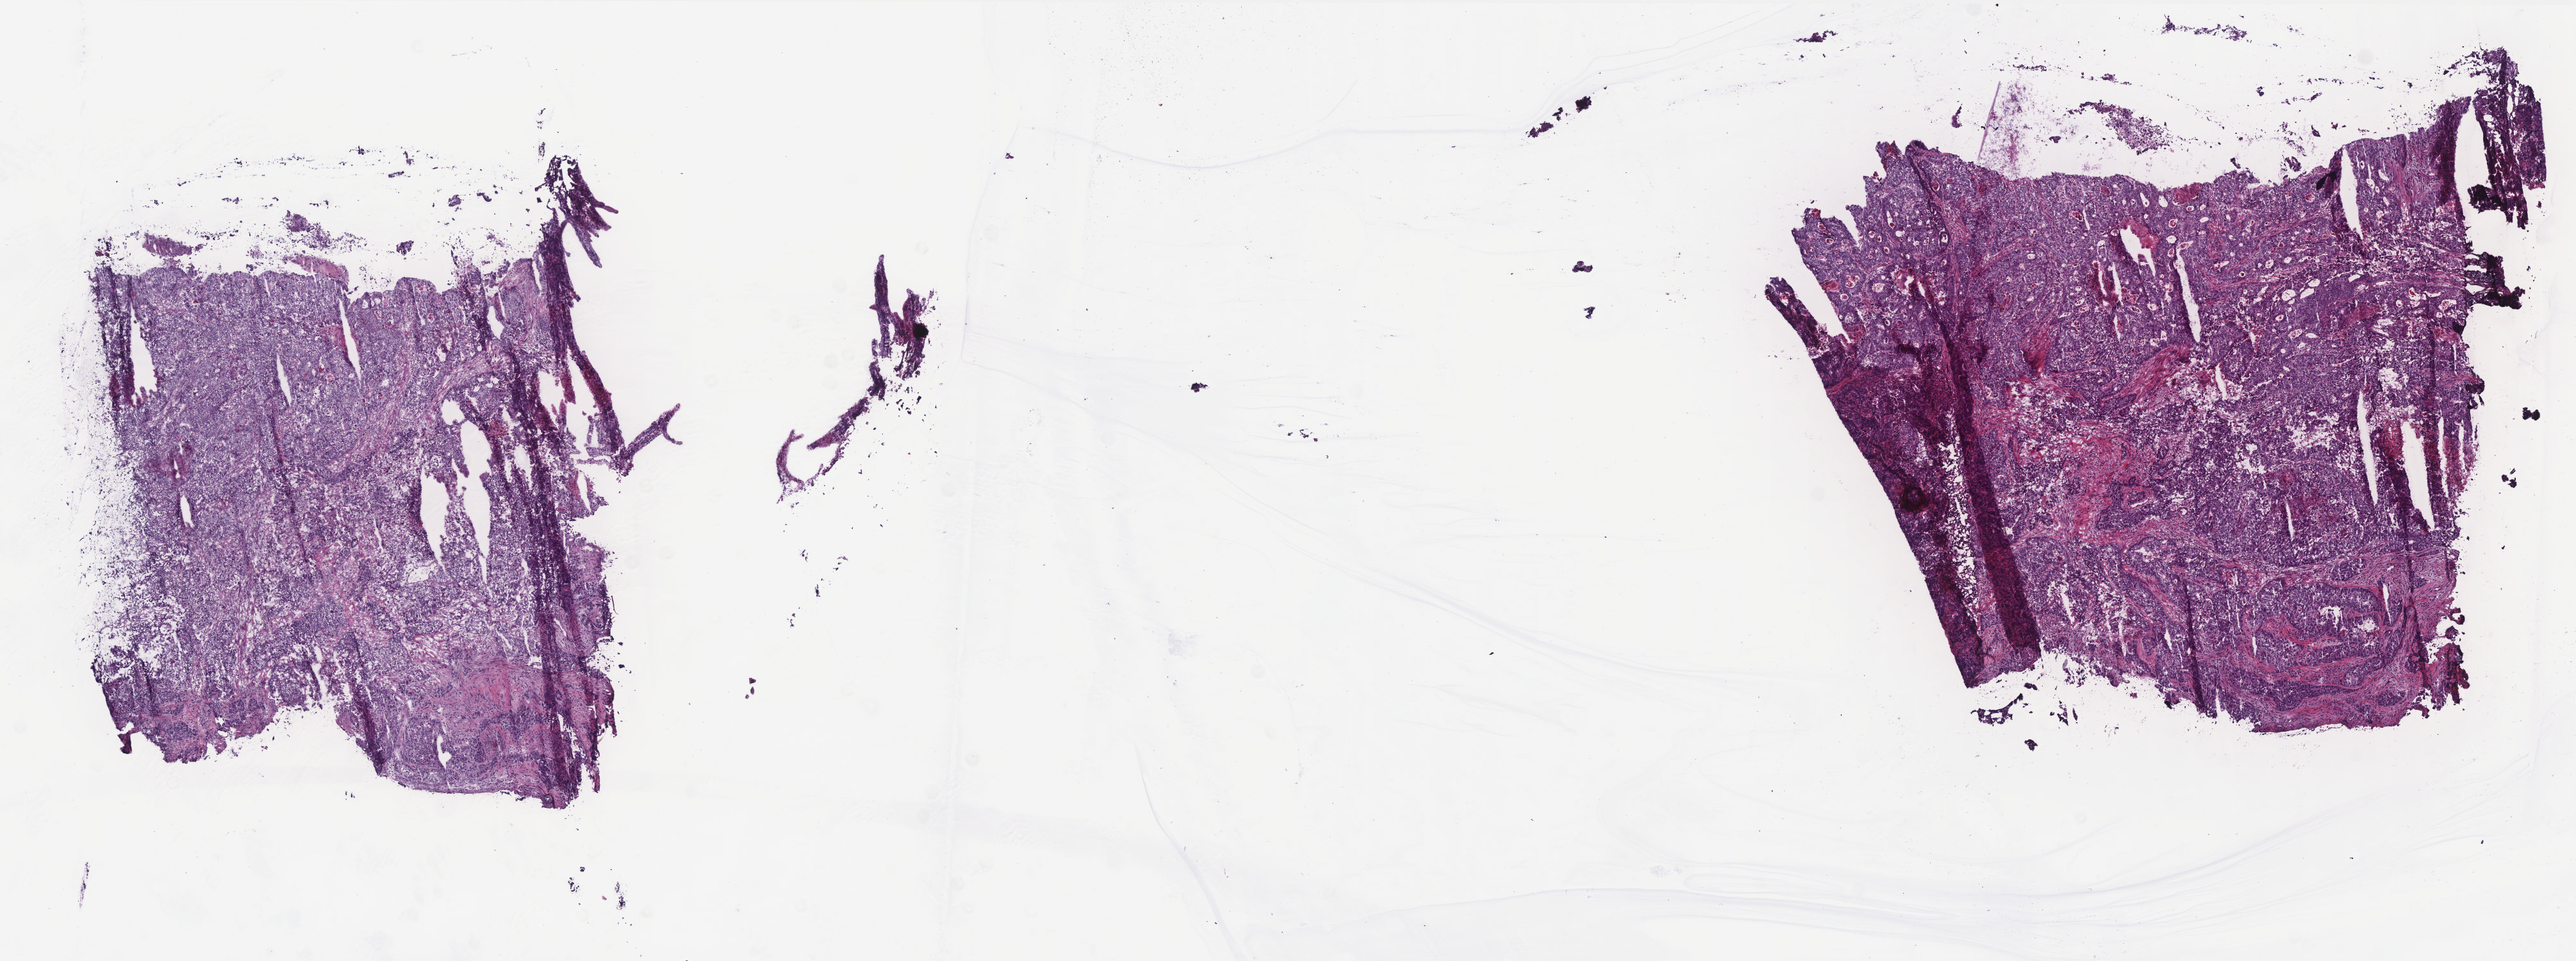
Hematoxylin and eosin (H&E) stained whole-slide image — shown as a low-resolution overview of the whole scanned area (about 16.1 x 6.0 mm). Frozen section from the top of the tissue portion. Sample: primary tumour, colon. Male, age 50 years at initial diagnosis. Composition of this section per pathologist review: tumour cells 80%, tumour nuclei 75%, normal cells 0%, stromal cells 13%, necrosis 7%. Infiltration values recorded for this section: lymphocyte infiltration 6%, monocyte infiltration 2%, neutrophil infiltration 6%.
• lymph nodes positive (case pathology): 7 of 20 examined
• TNM: T4 N2 M1
• histologic diagnosis: Adenocarcinoma, NOS (ascending colon)
• AJCC pathologic stage: IV (6th edition)